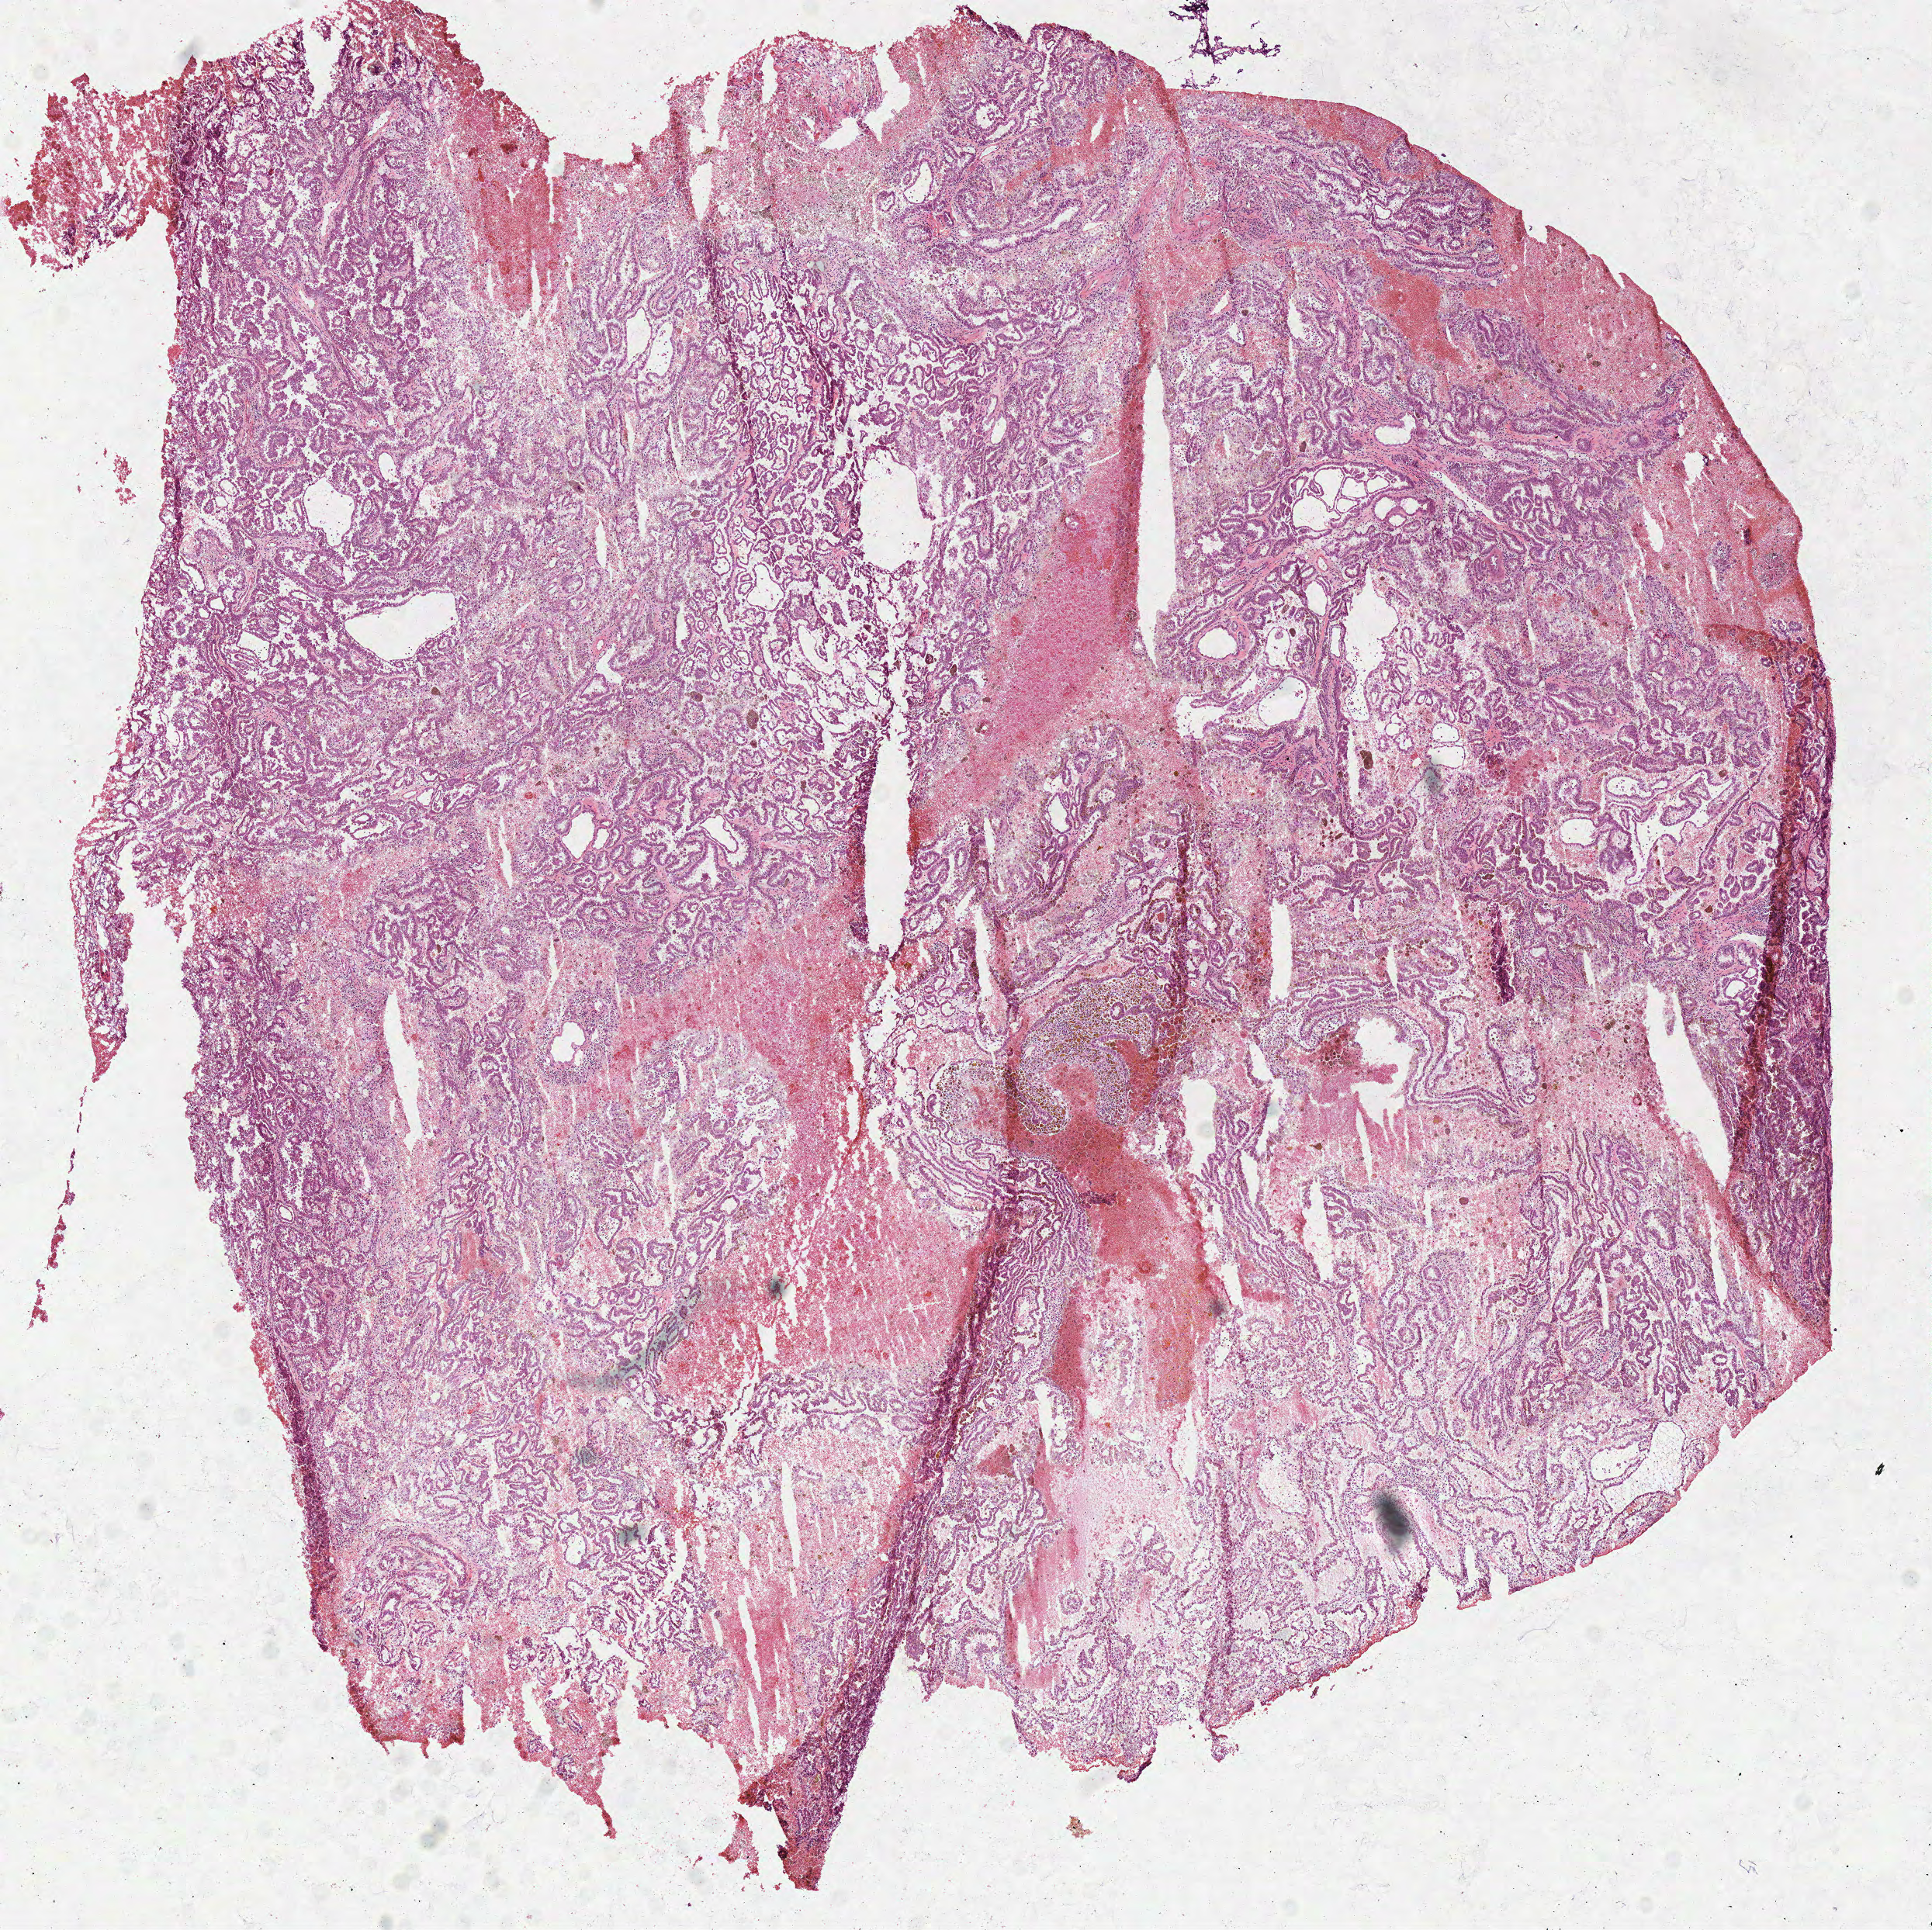
Digitized H&E-stained tissue section (whole slide) — low-resolution overview of the scanned area, about 9.8 x 9.8 mm; frozen section from the top of the tissue portion; primary tumour sample from the kidney. Male patient; age at initial diagnosis 57 years. Pathologist review of this section (percent, as recorded): tumour cells 84%, tumour nuclei 85%, normal cells 0%, stromal cells 1%, necrosis 15%.
AJCC pathologic stage: I. Diagnosis: Papillary adenocarcinoma, NOS.